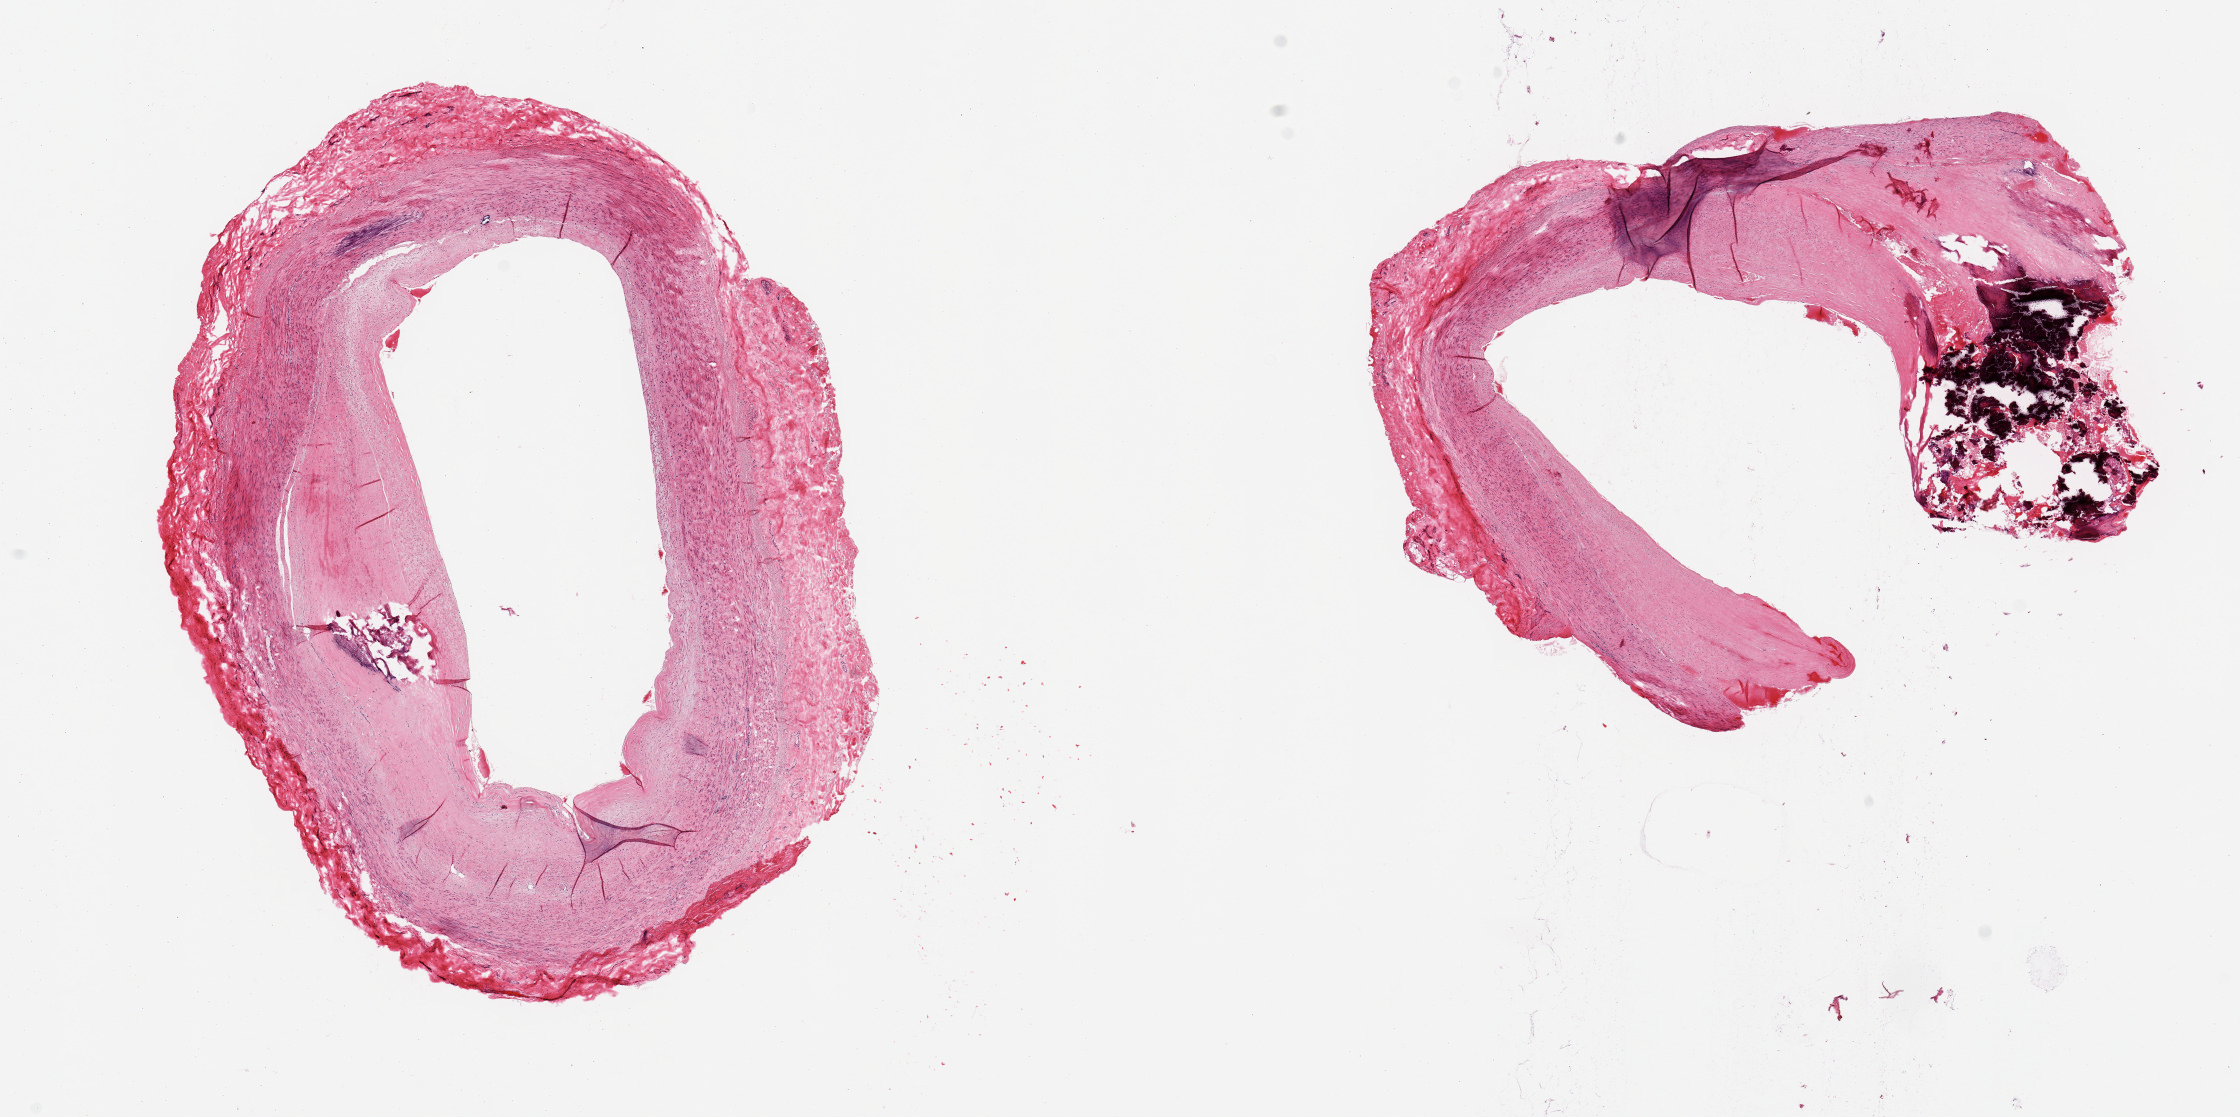
Whole-slide image, hematoxylin and eosin (H&E) stain — low-resolution overview of the scanned area, about 17.7 x 8.8 mm. PAXgene-fixed paraffin-embedded (PFPE) section. Sampled site (target tissue): tibial artery. Donor tissue sample. Donor sex: male.
- review note (as recorded): 2 pieces; calcific atherosclerosis and medial calcification